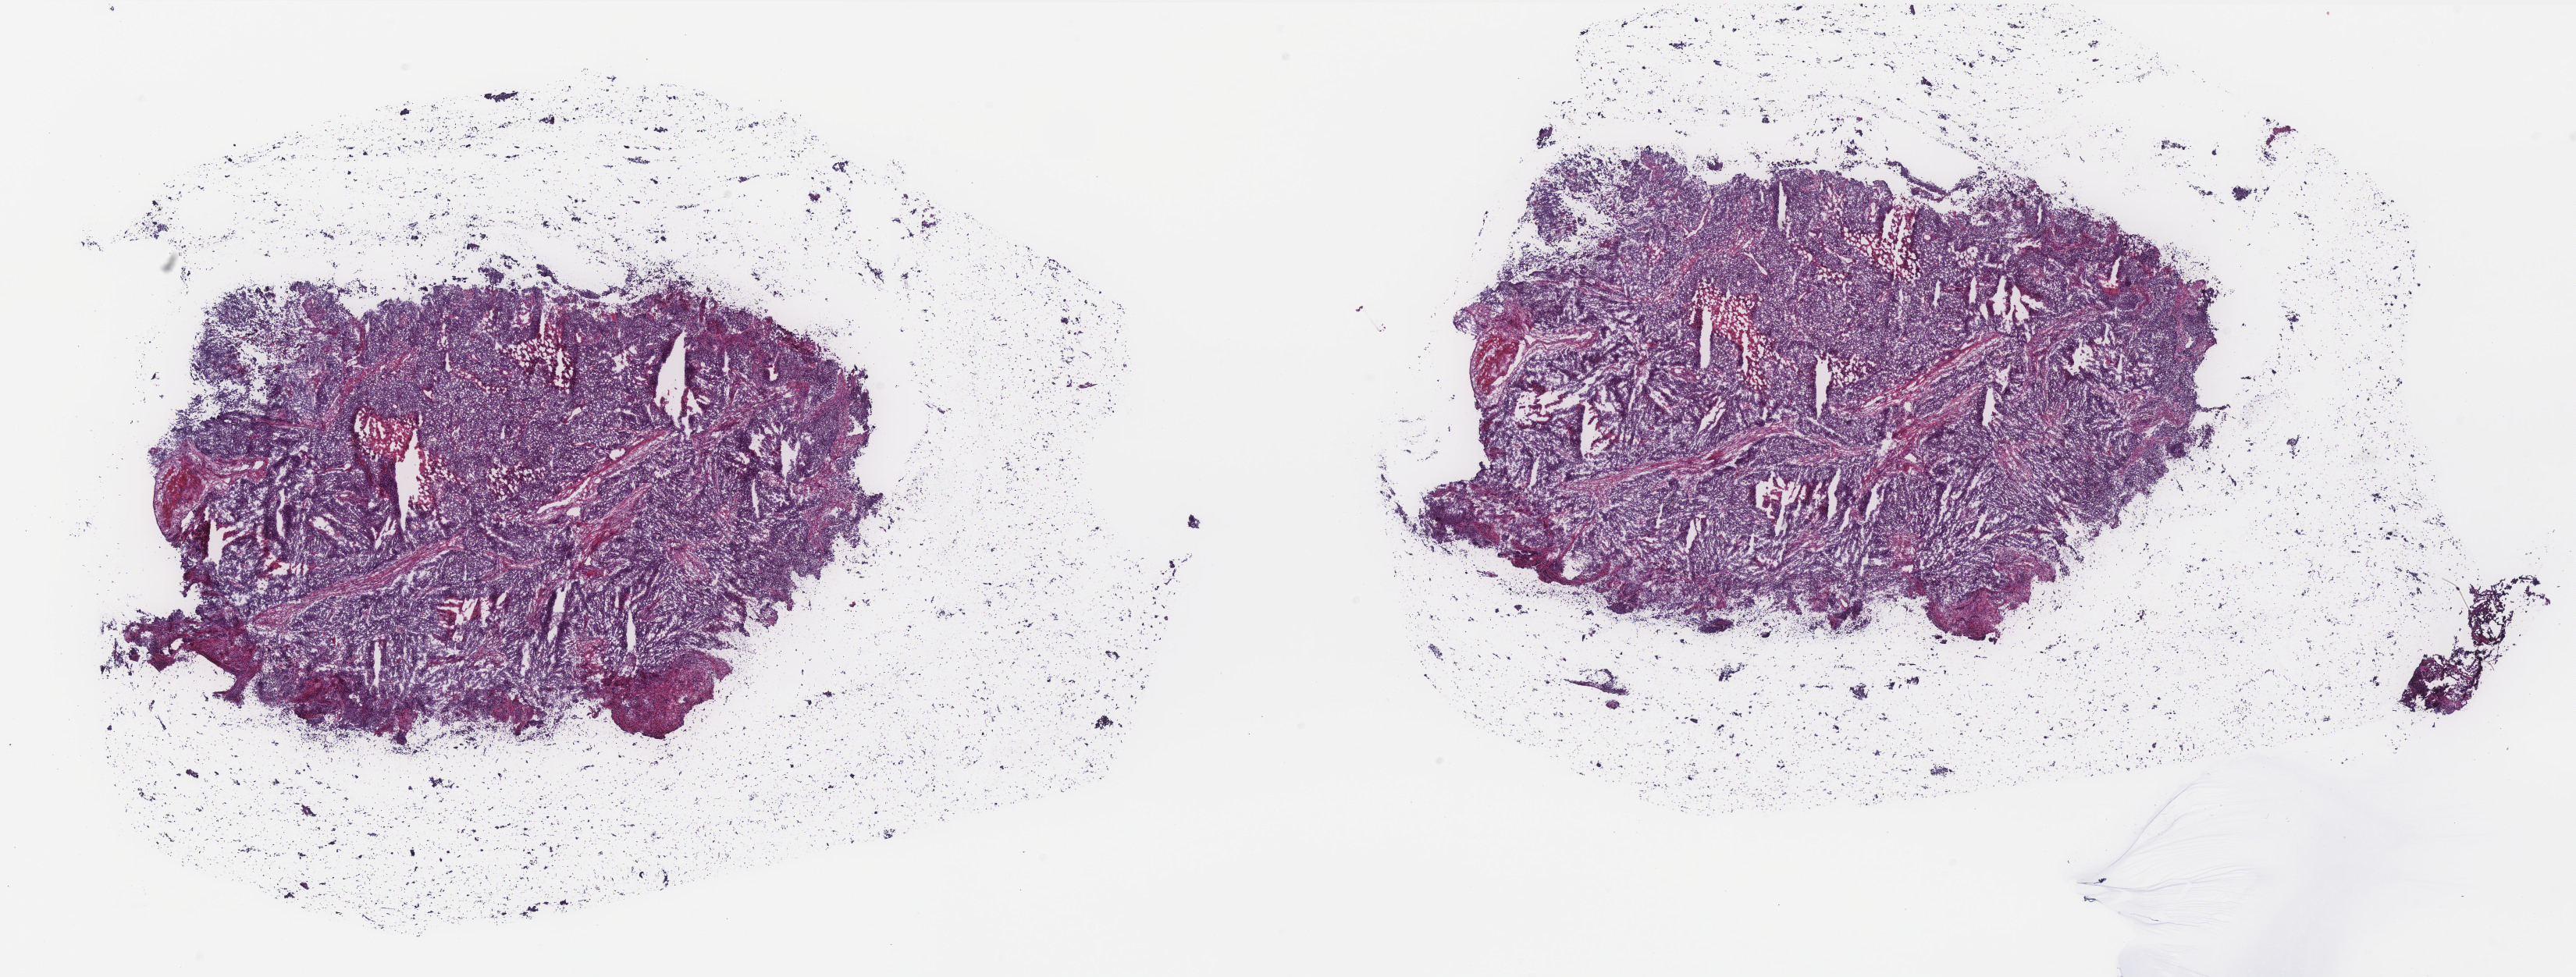
H&E whole-slide image — a low-resolution overview of the entire scanned area, about 26.5 x 10.0 mm (from a 40x scan); frozen section; sample: primary tumour, uterus. Female, age 56 years at initial diagnosis. Histologic grade: G3 (poorly differentiated). Pathologist review of this section (percent, as recorded): tumour cells 95%, tumour nuclei 85%, normal cells 0%, stromal cells 0%, necrosis 5%. Inflammatory infiltration, as recorded: lymphocyte infiltration 0%, monocyte infiltration 0%, neutrophil infiltration 0%.
- FIGO stage: IIIC
- pathologic diagnosis: Endometrioid adenocarcinoma, NOS (endometrium)